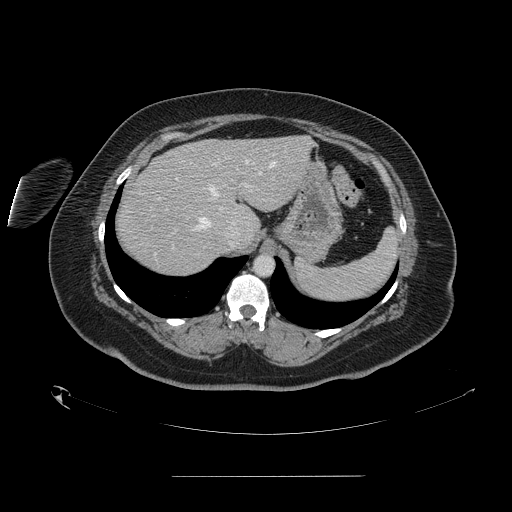
Contrast-enhanced abdominal CT, one axial slice; slice 117 of 164 in the series (ordered by position); 120 kVp; intravenous contrast given; soft-tissue window (W 400 / L 40 HU); 2.5 mm slice thickness; 512 × 512 image matrix. Female patient, age 52 years. From the clinical record (not read from this slice): diagnosis: colorectal cancer liver metastases, imaged before liver resection; multiple liver metastases: yes; largest metastasis: 3.5 cm; disease in both lobes: no.
Annotated regions visible in this slice (manually delineated by an expert):
- hepatic veins: bounding box [x1, y1, x2, y2] px = [172, 159, 275, 246]
- liver: [116, 136, 312, 276]
- planned liver remnant (the part of the liver to remain after resection): [169, 136, 312, 226]
- portal vein (with intrahepatic branches): [175, 178, 247, 210]